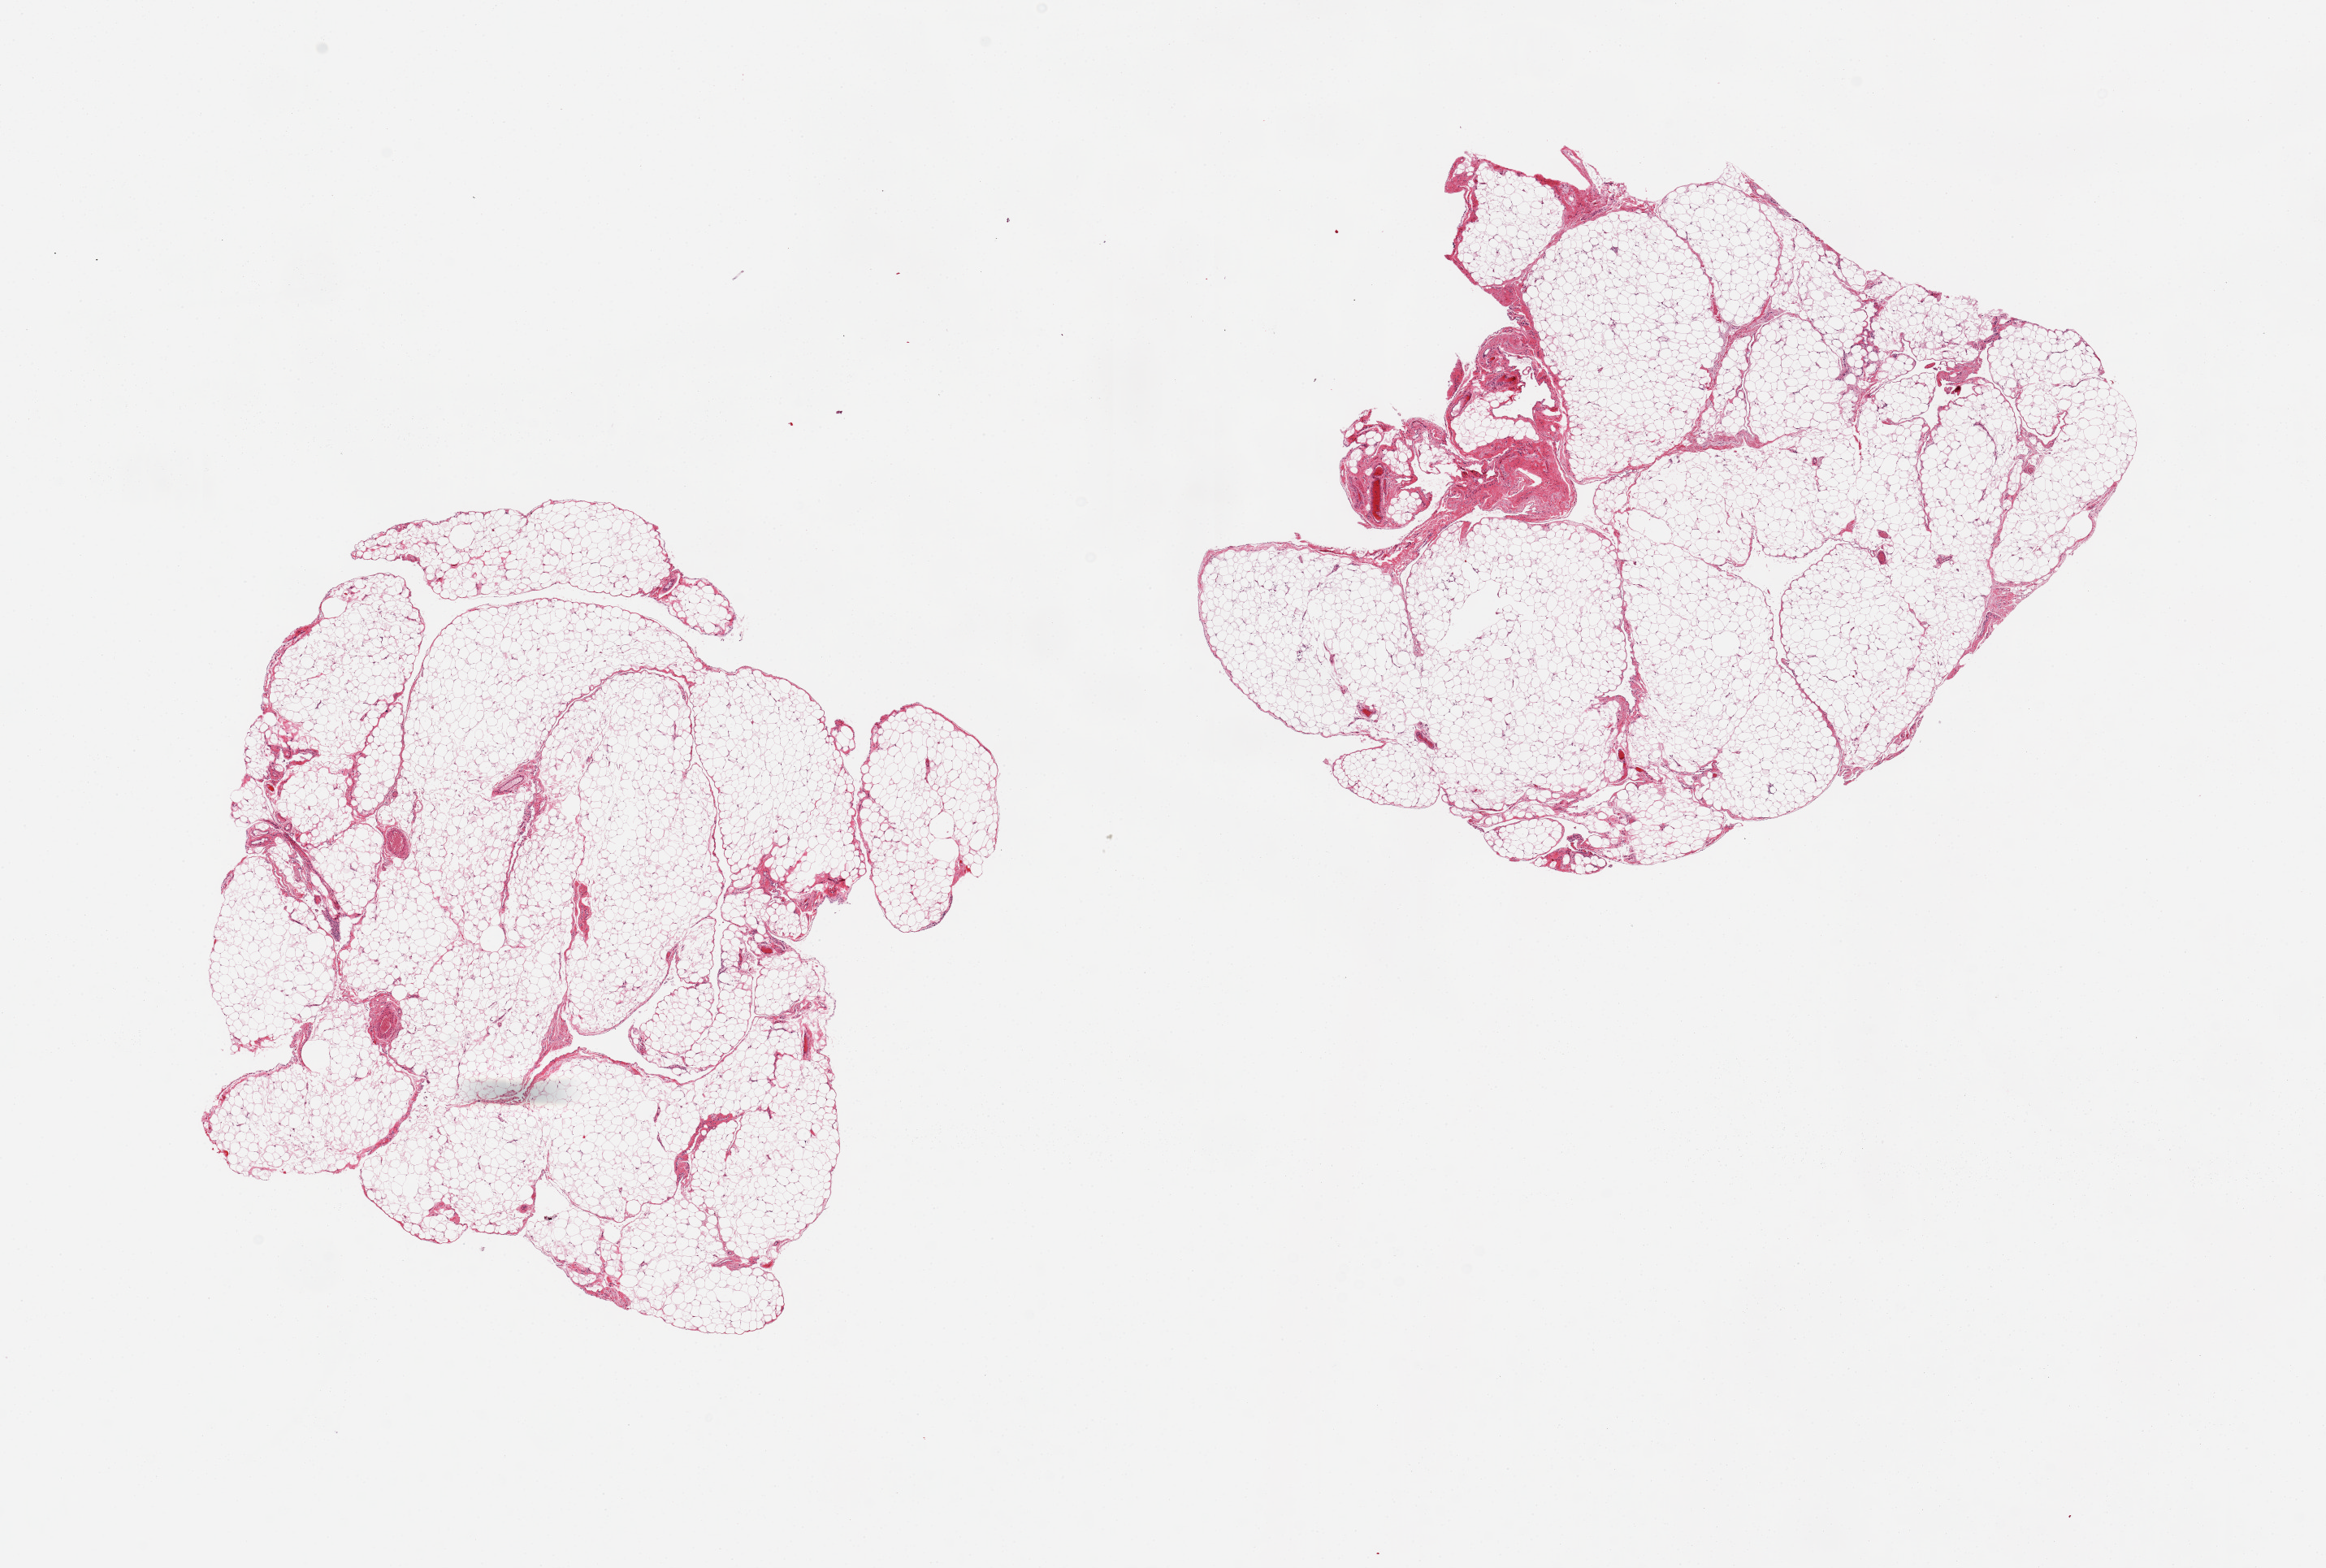
Haematoxylin and eosin whole-slide image — whole scanned area (about 22.6 x 15.3 mm, from a 20x scan) shown as a low-resolution overview; PAXgene-fixed, paraffin-embedded tissue; section of omentum (target tissue); tissue donor sample. Donor: male.
Review note (as recorded): 2 pieces, mld mesothelial hyperplasia/fibrosis.